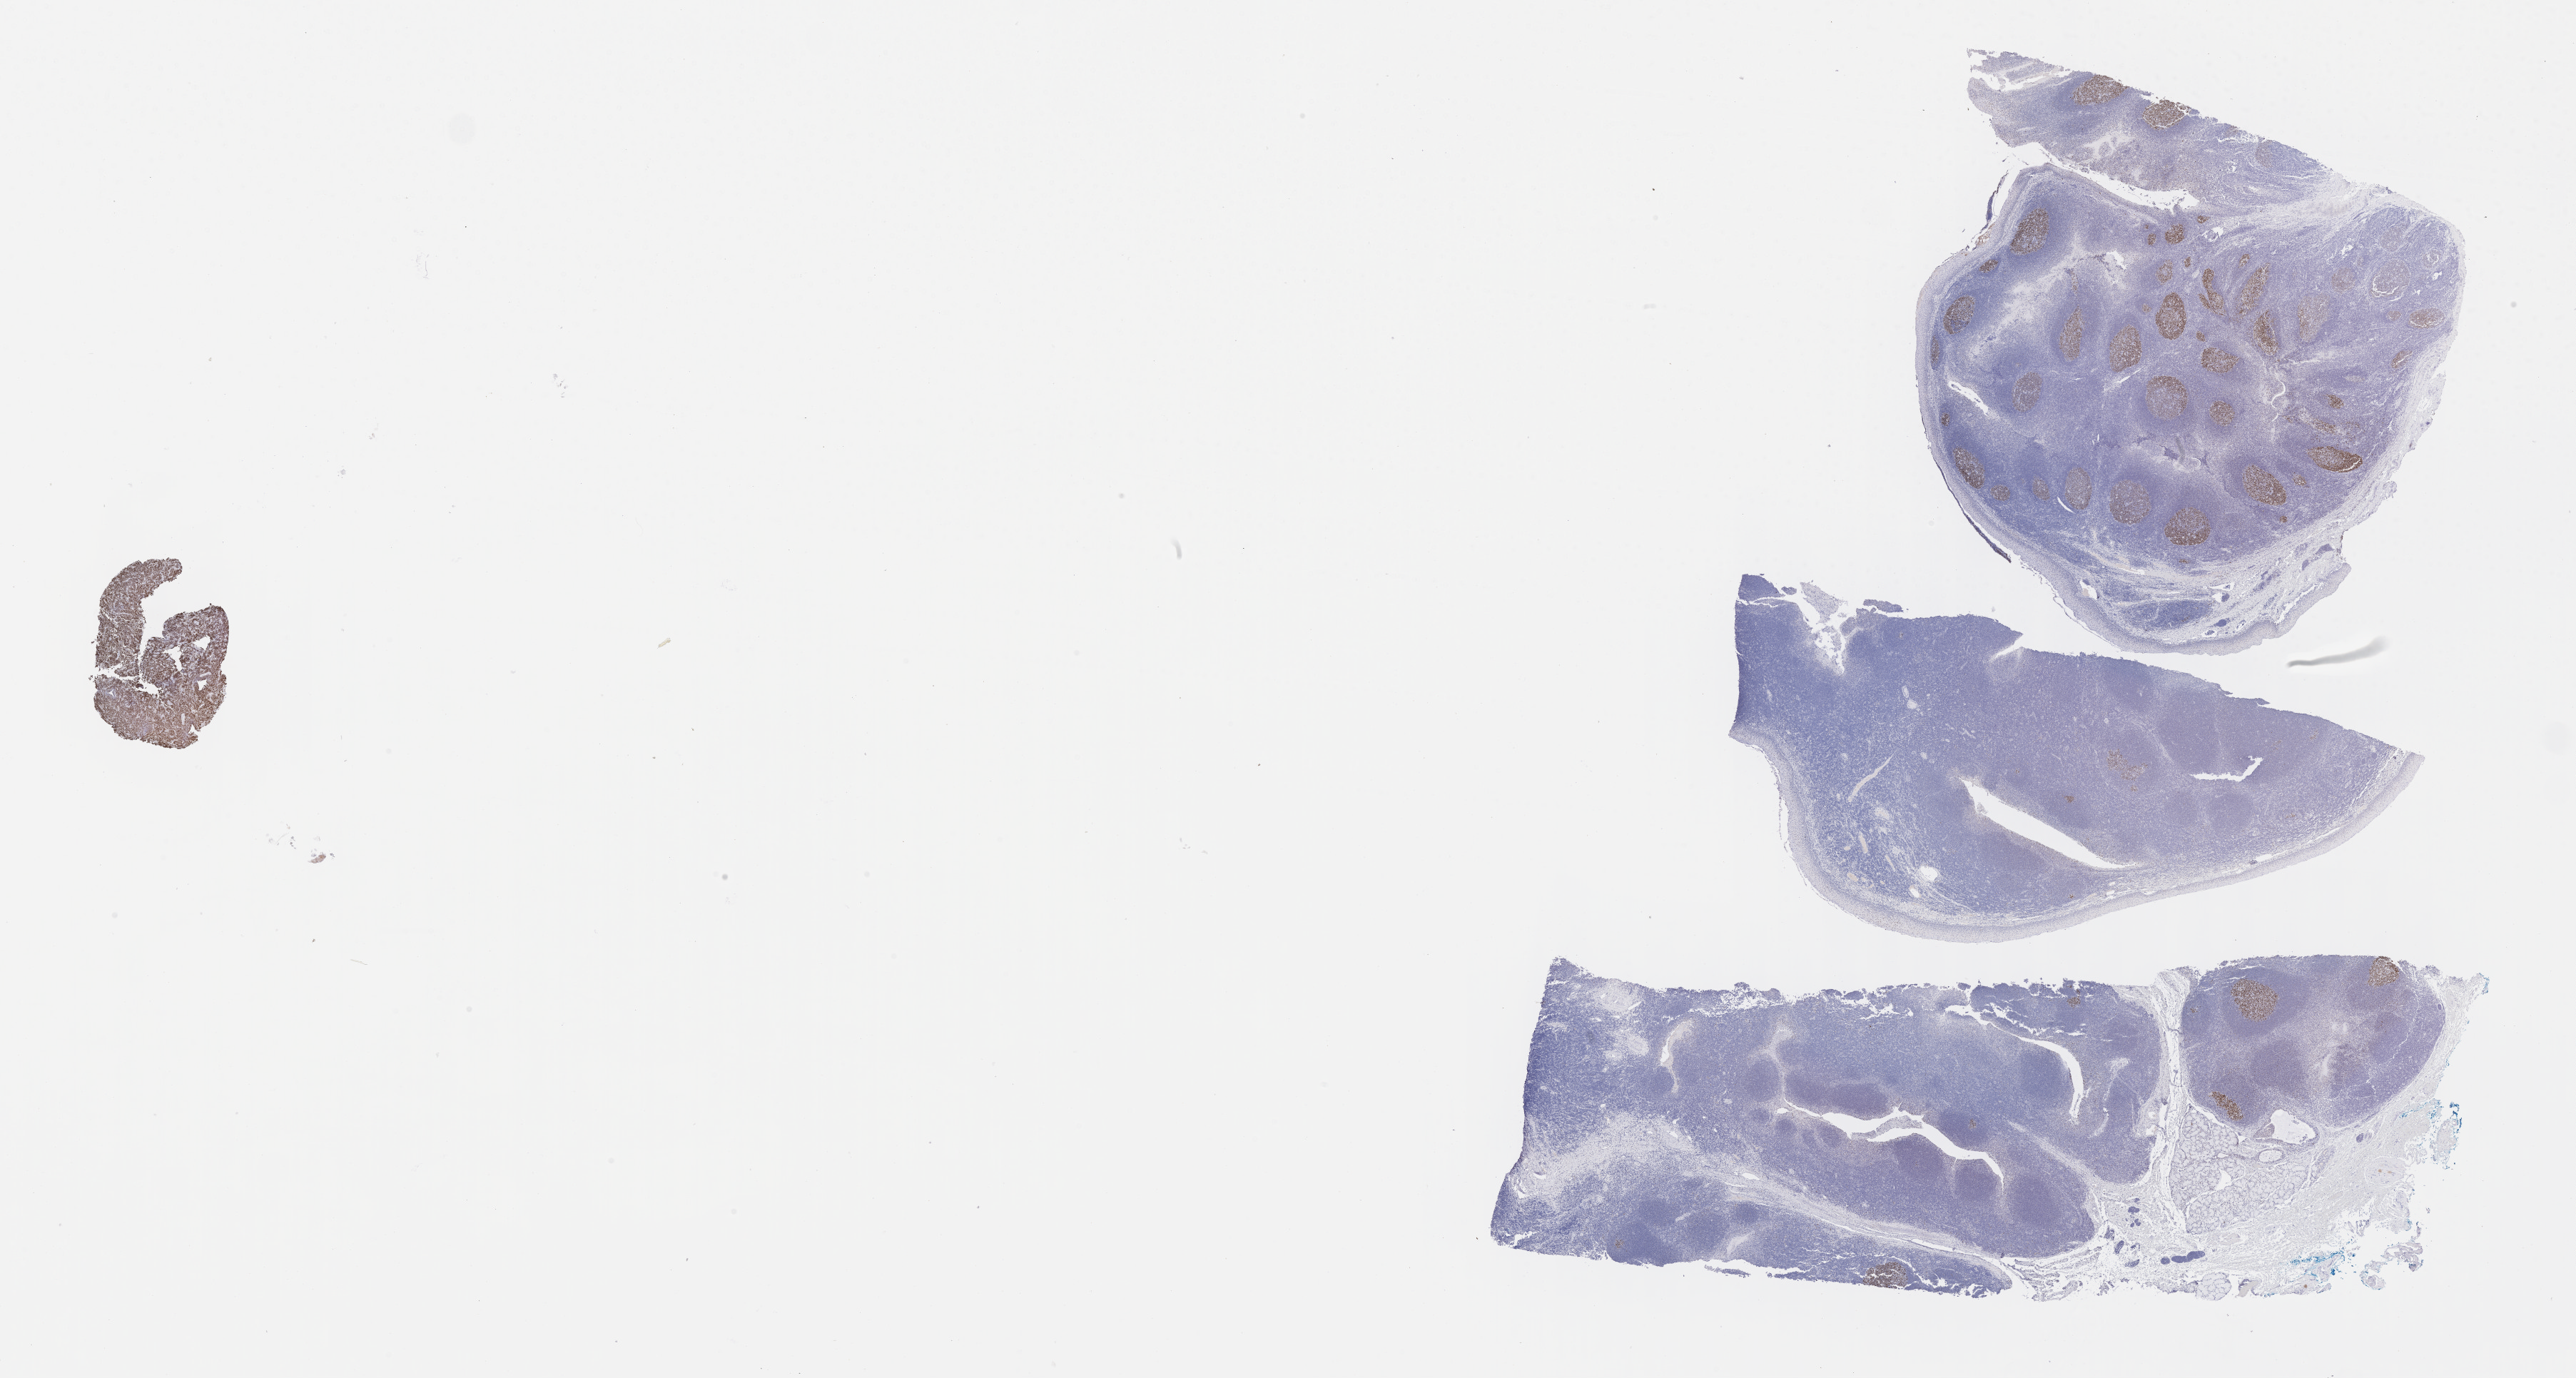
Immunohistochemistry (IHC) whole-slide image stained for BCL6, shown as a low-resolution overview of the whole scanned area (about 29.2 x 15.6 mm), tumor tissue. Patient: female, age at initial diagnosis 8 years.
Histologic diagnosis: Burkitt lymphoma, NOS.